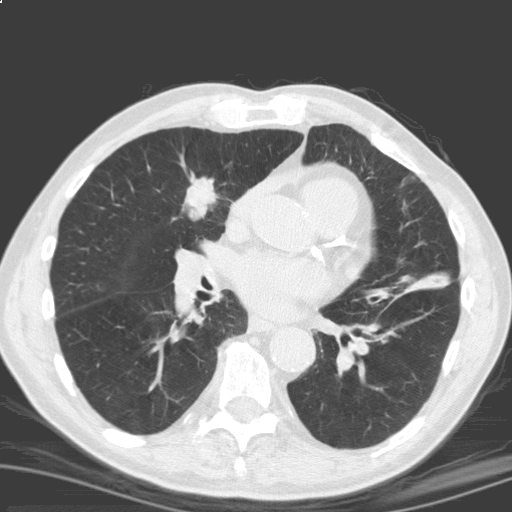
Chest CT (low-dose screening protocol), one axial image; second screening round (one year after baseline); lung window (W 1500 / L -600 HU); 3.2 mm slice thickness; 120 kVp; slice 93 of 184 in the series; 512 × 512 image matrix, field of view 329 × 329 mm. Male, age 69 years at enrolment. Current smoker at enrolment.
- Expert reader's lesion annotation, bounding box [x1, y1, x2, y2] px = [168, 163, 232, 225].
- The screening reader recorded 2 non-calcified nodules or masses ≥4 mm on this exam (right upper lobe, left lower lobe); which of them this box marks is not recorded.
- Official screen result: positive, other.
- Participant outcome: lung cancer diagnosed 17 days after this screen — squamous cell carcinoma, NOS, right upper lobe, moderately differentiated (G2), stage IB (AJCC 6th edition), 40 mm at pathology.